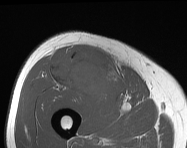
MRI of an extremity soft-tissue mass, one axial slice; slice 73 of 114 in the series (ordered by position); MR volume resampled by the dataset authors to the PET/CT grid (not the native acquisition matrix); 187 × 148 image matrix. Male patient. From the clinical record (not read from this slice): histological type: pleiomorphic leiomyosarcoma; grade: intermediate; site of the primary tumour: right thigh.
Structures marked on this image (expert contour drawn on MRI and transferred to this co-registered scan by the dataset authors):
- gross tumour volume including surrounding oedema: bounding box (x1, y1, x2, y2) in pixels: (52, 47, 115, 96)
- gross tumour volume (mass): (52, 50, 115, 96)